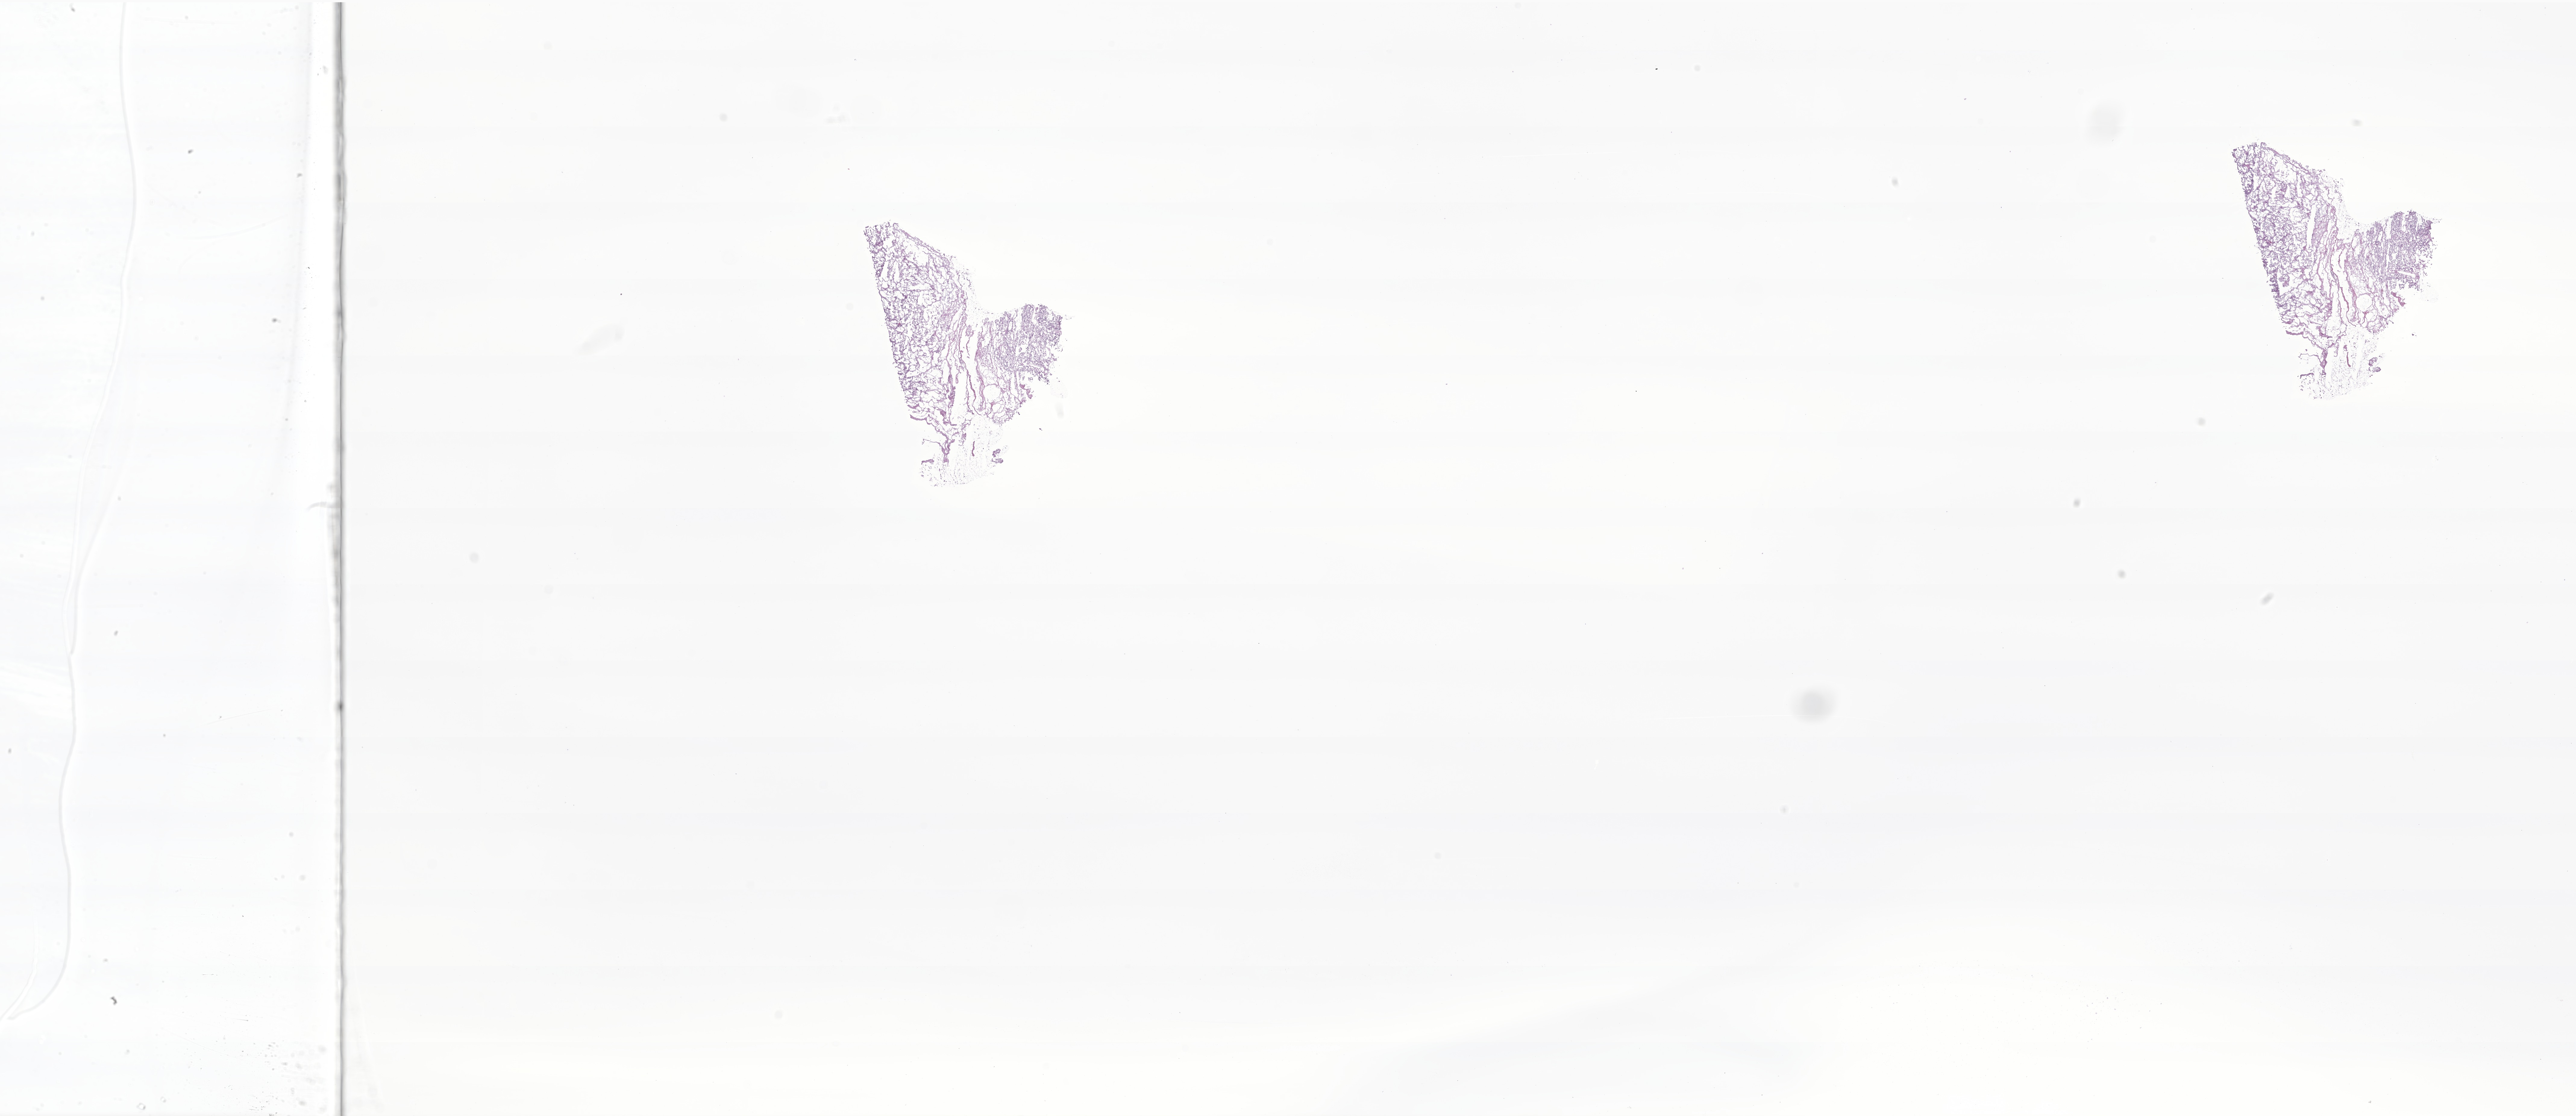
H&E whole-slide image of tumor tissue from the thyroid, shown as a low-resolution overview of the whole scanned area (about 36.0 x 15.6 mm), cryosection (OCT / tissue freezing medium). Patient female; age 181 months (15 years 1 month).
- diagnosis (ICD-O-3 morphology term): Carcinoma, NOS